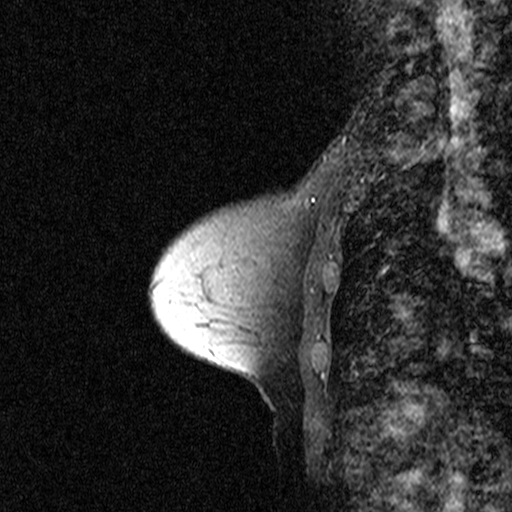
Breast MRI (dynamic contrast-enhanced), one sagittal slice; slice 16 of 44 in the series (ordered by position); dynamic contrast-enhanced study with each time point stored as its own series, time point 2 of 3 at this slice position (early post-contrast, ordered by acquisition time); 1.5 T; TE 4.5 ms, TR 11 ms; 2.27 mm slice thickness; 512 × 512 image matrix, field of view 200 × 200 mm. Patient: female, 53 years. Case-level facts recorded for this patient, not image findings: setting: breast cancer imaged before/during neoadjuvant chemotherapy; receptor status: HR-positive, HER2-negative.
Outlined on this slice (semi-automatically segmented with operator editing):
- analysis volume of interest (the breast-tissue region the enhancement analysis was run in; not a lesion): bounding box [x1, y1, x2, y2] px = [200, 178, 317, 309]
- tumour enhancement mask (voxels above the 90 % enhancement threshold inside the analysis volume of interest): [308, 199, 314, 205]